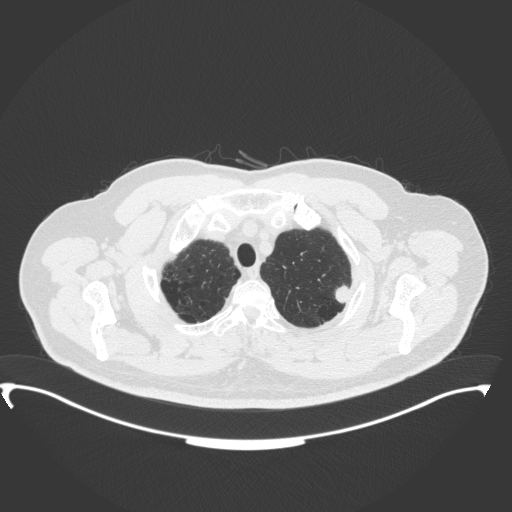
Chest CT, one axial slice. Position 323 of 350 along the scan axis. Reconstruction kernel B31f. Lung window (W 1500 / L -600 HU). 1 mm slice thickness. 512 × 512 image matrix. Patient: male, 64 years. From the clinical record (not read from this slice): clinical TNM (as recorded): T1c N1 M1.
Outlined on this slice (bounding box drawn by a radiologist):
- lung tumour (recorded histology: adenocarcinoma): bounding box [x1, y1, x2, y2] px = [334, 285, 353, 305]